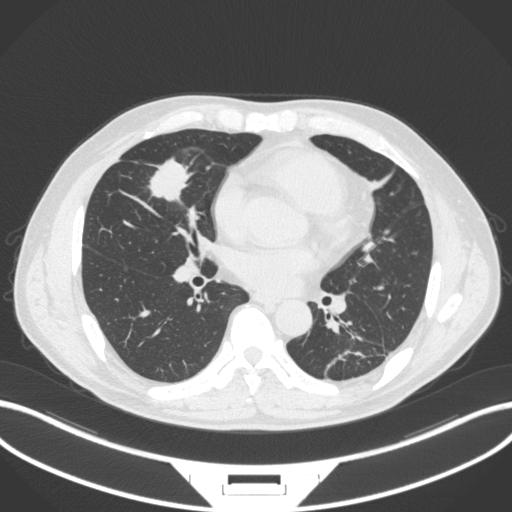
Chest CT, one axial slice; slice 139 of 399 in the series (ordered by position); lung window (W 1500 / L -600 HU); 512 × 512 image matrix. Male patient, age 59 years. From the clinical record (not read from this slice): clinical TNM (as recorded): T2a N1 M0.
Structures marked on this image (rectangle marked by the reading radiologist):
- lung tumour (recorded histology: adenocarcinoma): bounding box (x1, y1, x2, y2) in pixels: (148, 157, 197, 205)